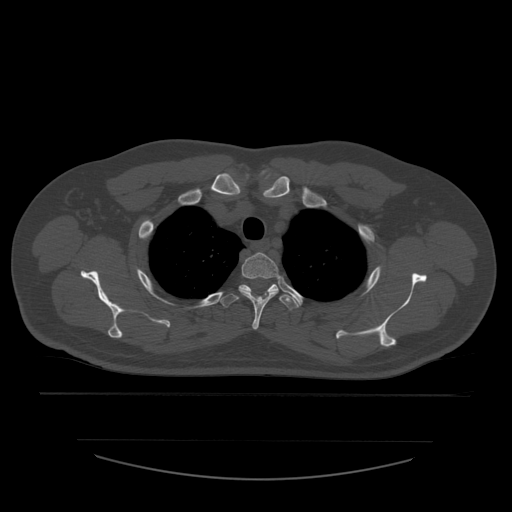
CT including the spine, one axial slice. Slice 444 of 532 in the series (ordered by position). Reconstruction kernel STANDARD. Bone window (W 1800 / L 400 HU). 512 × 512 image matrix, field of view 441 × 441 mm. Patient age 44 years. Case-level facts recorded for this patient, not image findings: primary cancer: soft tissue sarcoma.
Outlined on this slice (semi-automatic segmentation, software-assisted and operator-edited):
- T2 vertebra: bounding box [x1, y1, x2, y2] px = [239, 253, 280, 330]
- T3 vertebra: [220, 284, 299, 310]